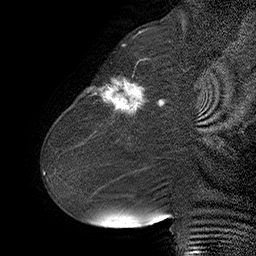
Breast MRI (dynamic contrast-enhanced), one sagittal slice. Position 22 of 55 along the scan axis. Dynamic contrast-enhanced series, time point 2 of 6 at this slice position (early post-contrast). 1.5 T. TE 4.5 ms, TR 32.4 ms. 3 mm slice thickness. 256 × 256 image matrix, field of view 180 × 180 mm. Female patient. From the clinical record (not read from this slice): setting: breast cancer imaged before/during neoadjuvant chemotherapy; receptor status: HER2-positive.
Structures marked on this image (semi-automatically segmented with operator editing):
- analysis volume of interest (the breast-tissue region the enhancement analysis was run in; not a lesion): box from (x=80, y=64) to (x=163, y=134) px
- tumour enhancement mask (voxels above the 100 % enhancement threshold inside the analysis volume of interest): (x=87, y=79)–(x=163, y=114)